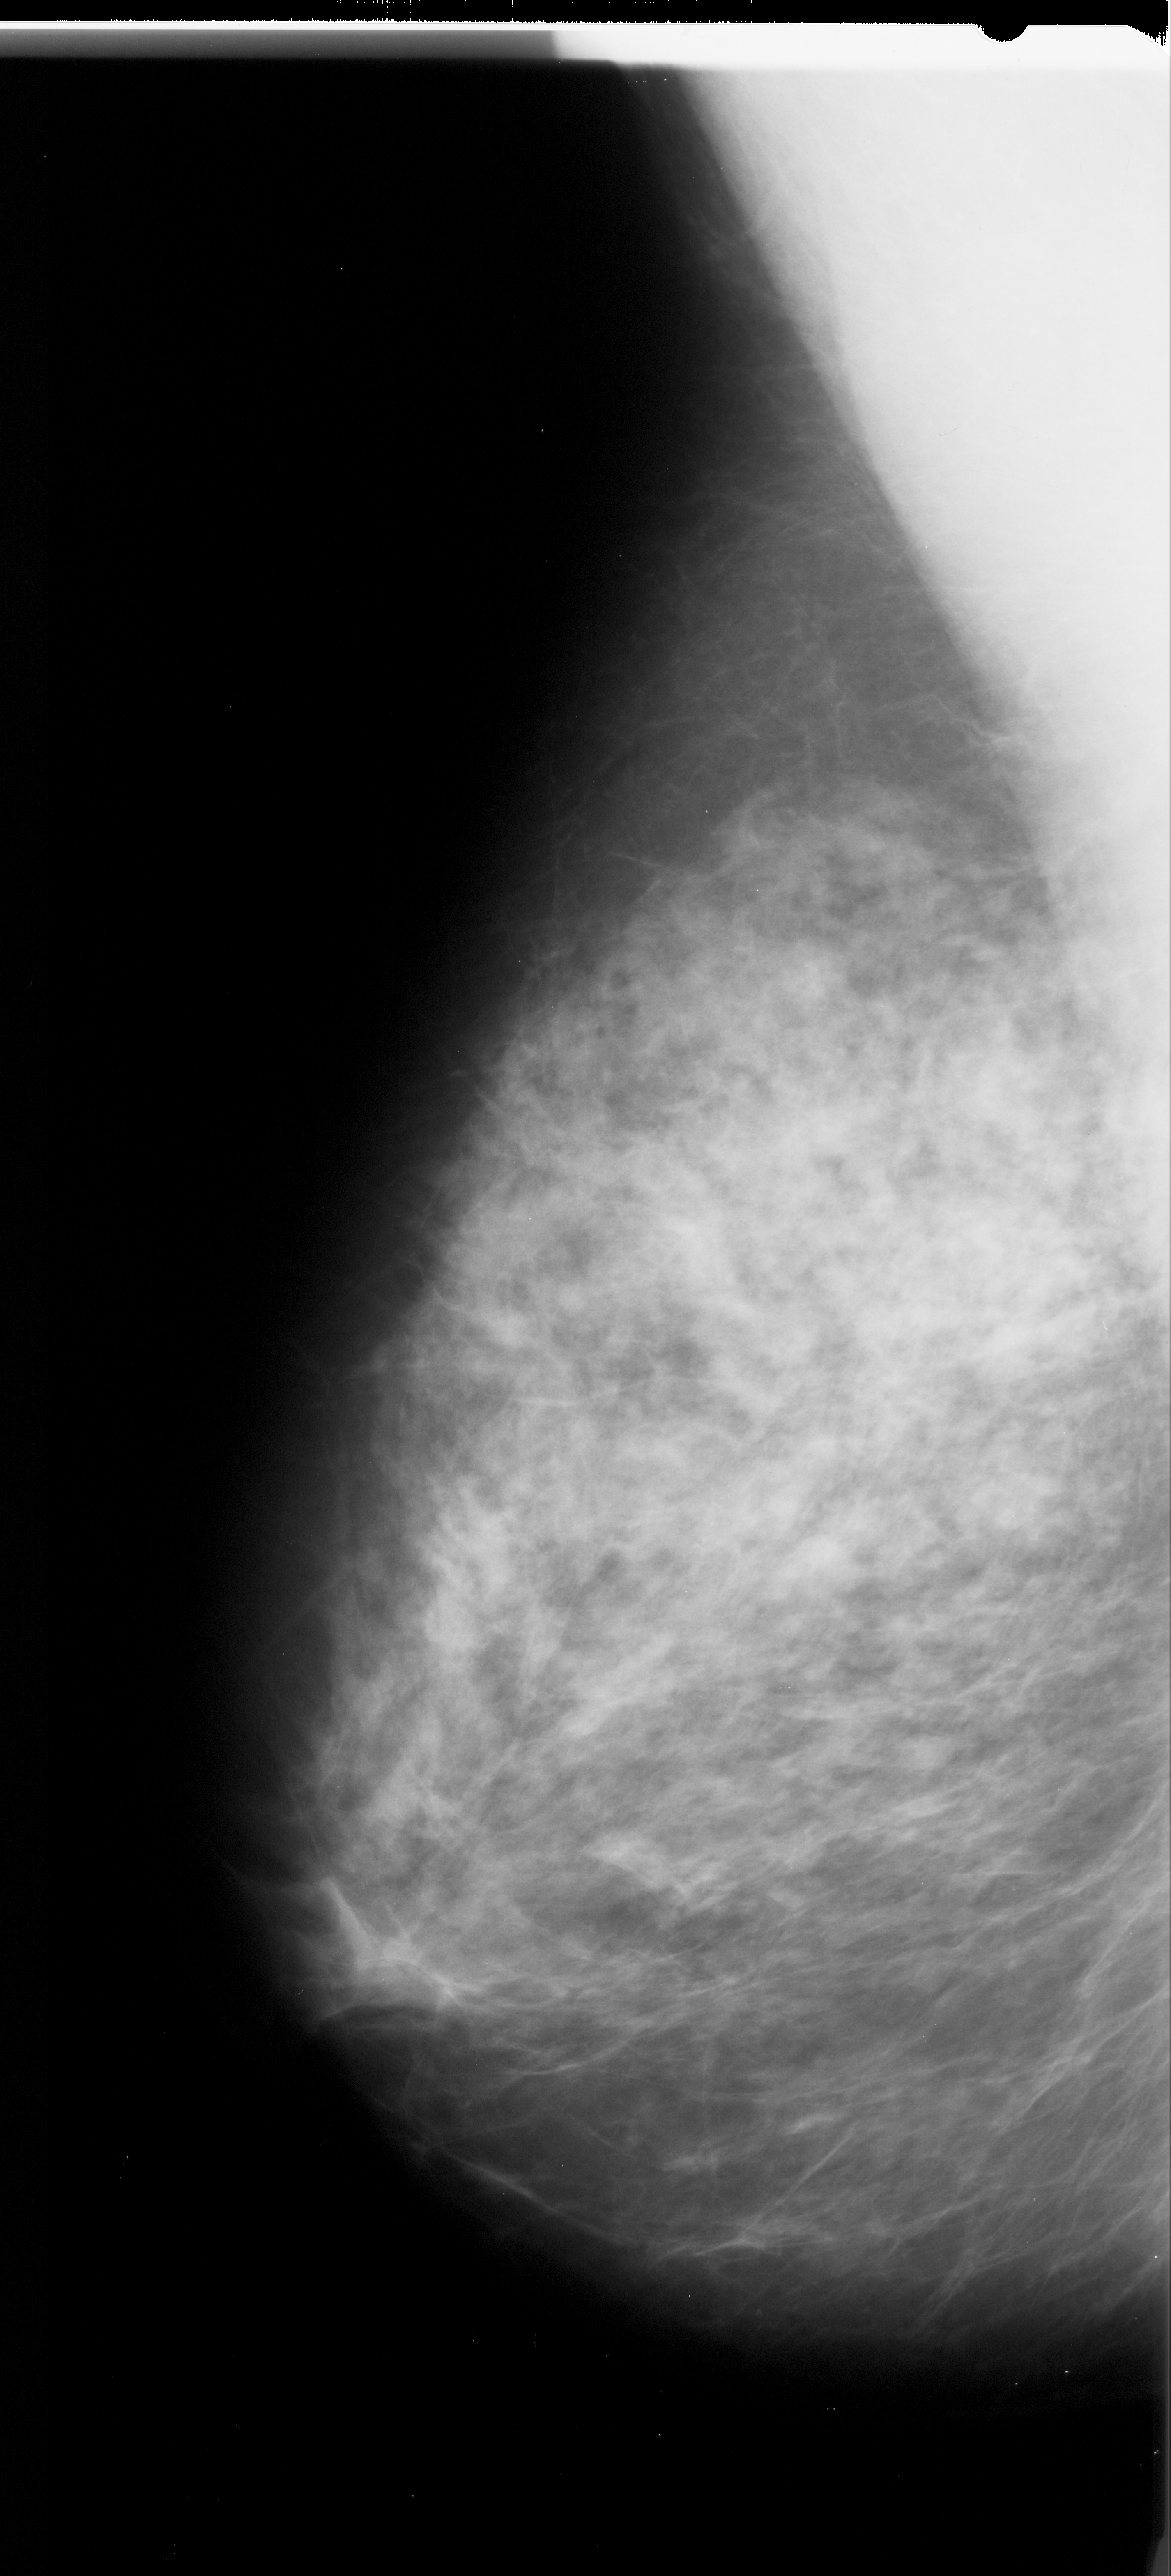
Scanned film-screen mammogram, left breast, mediolateral oblique (MLO) view.
Marked abnormality: calcifications, morphology pleomorphic, distribution clustered; BI-RADS assessment category 4; subtlety rating 1 on a 1 (subtle) to 5 (obvious) scale; pathology result (as recorded, not read from the image): malignant.